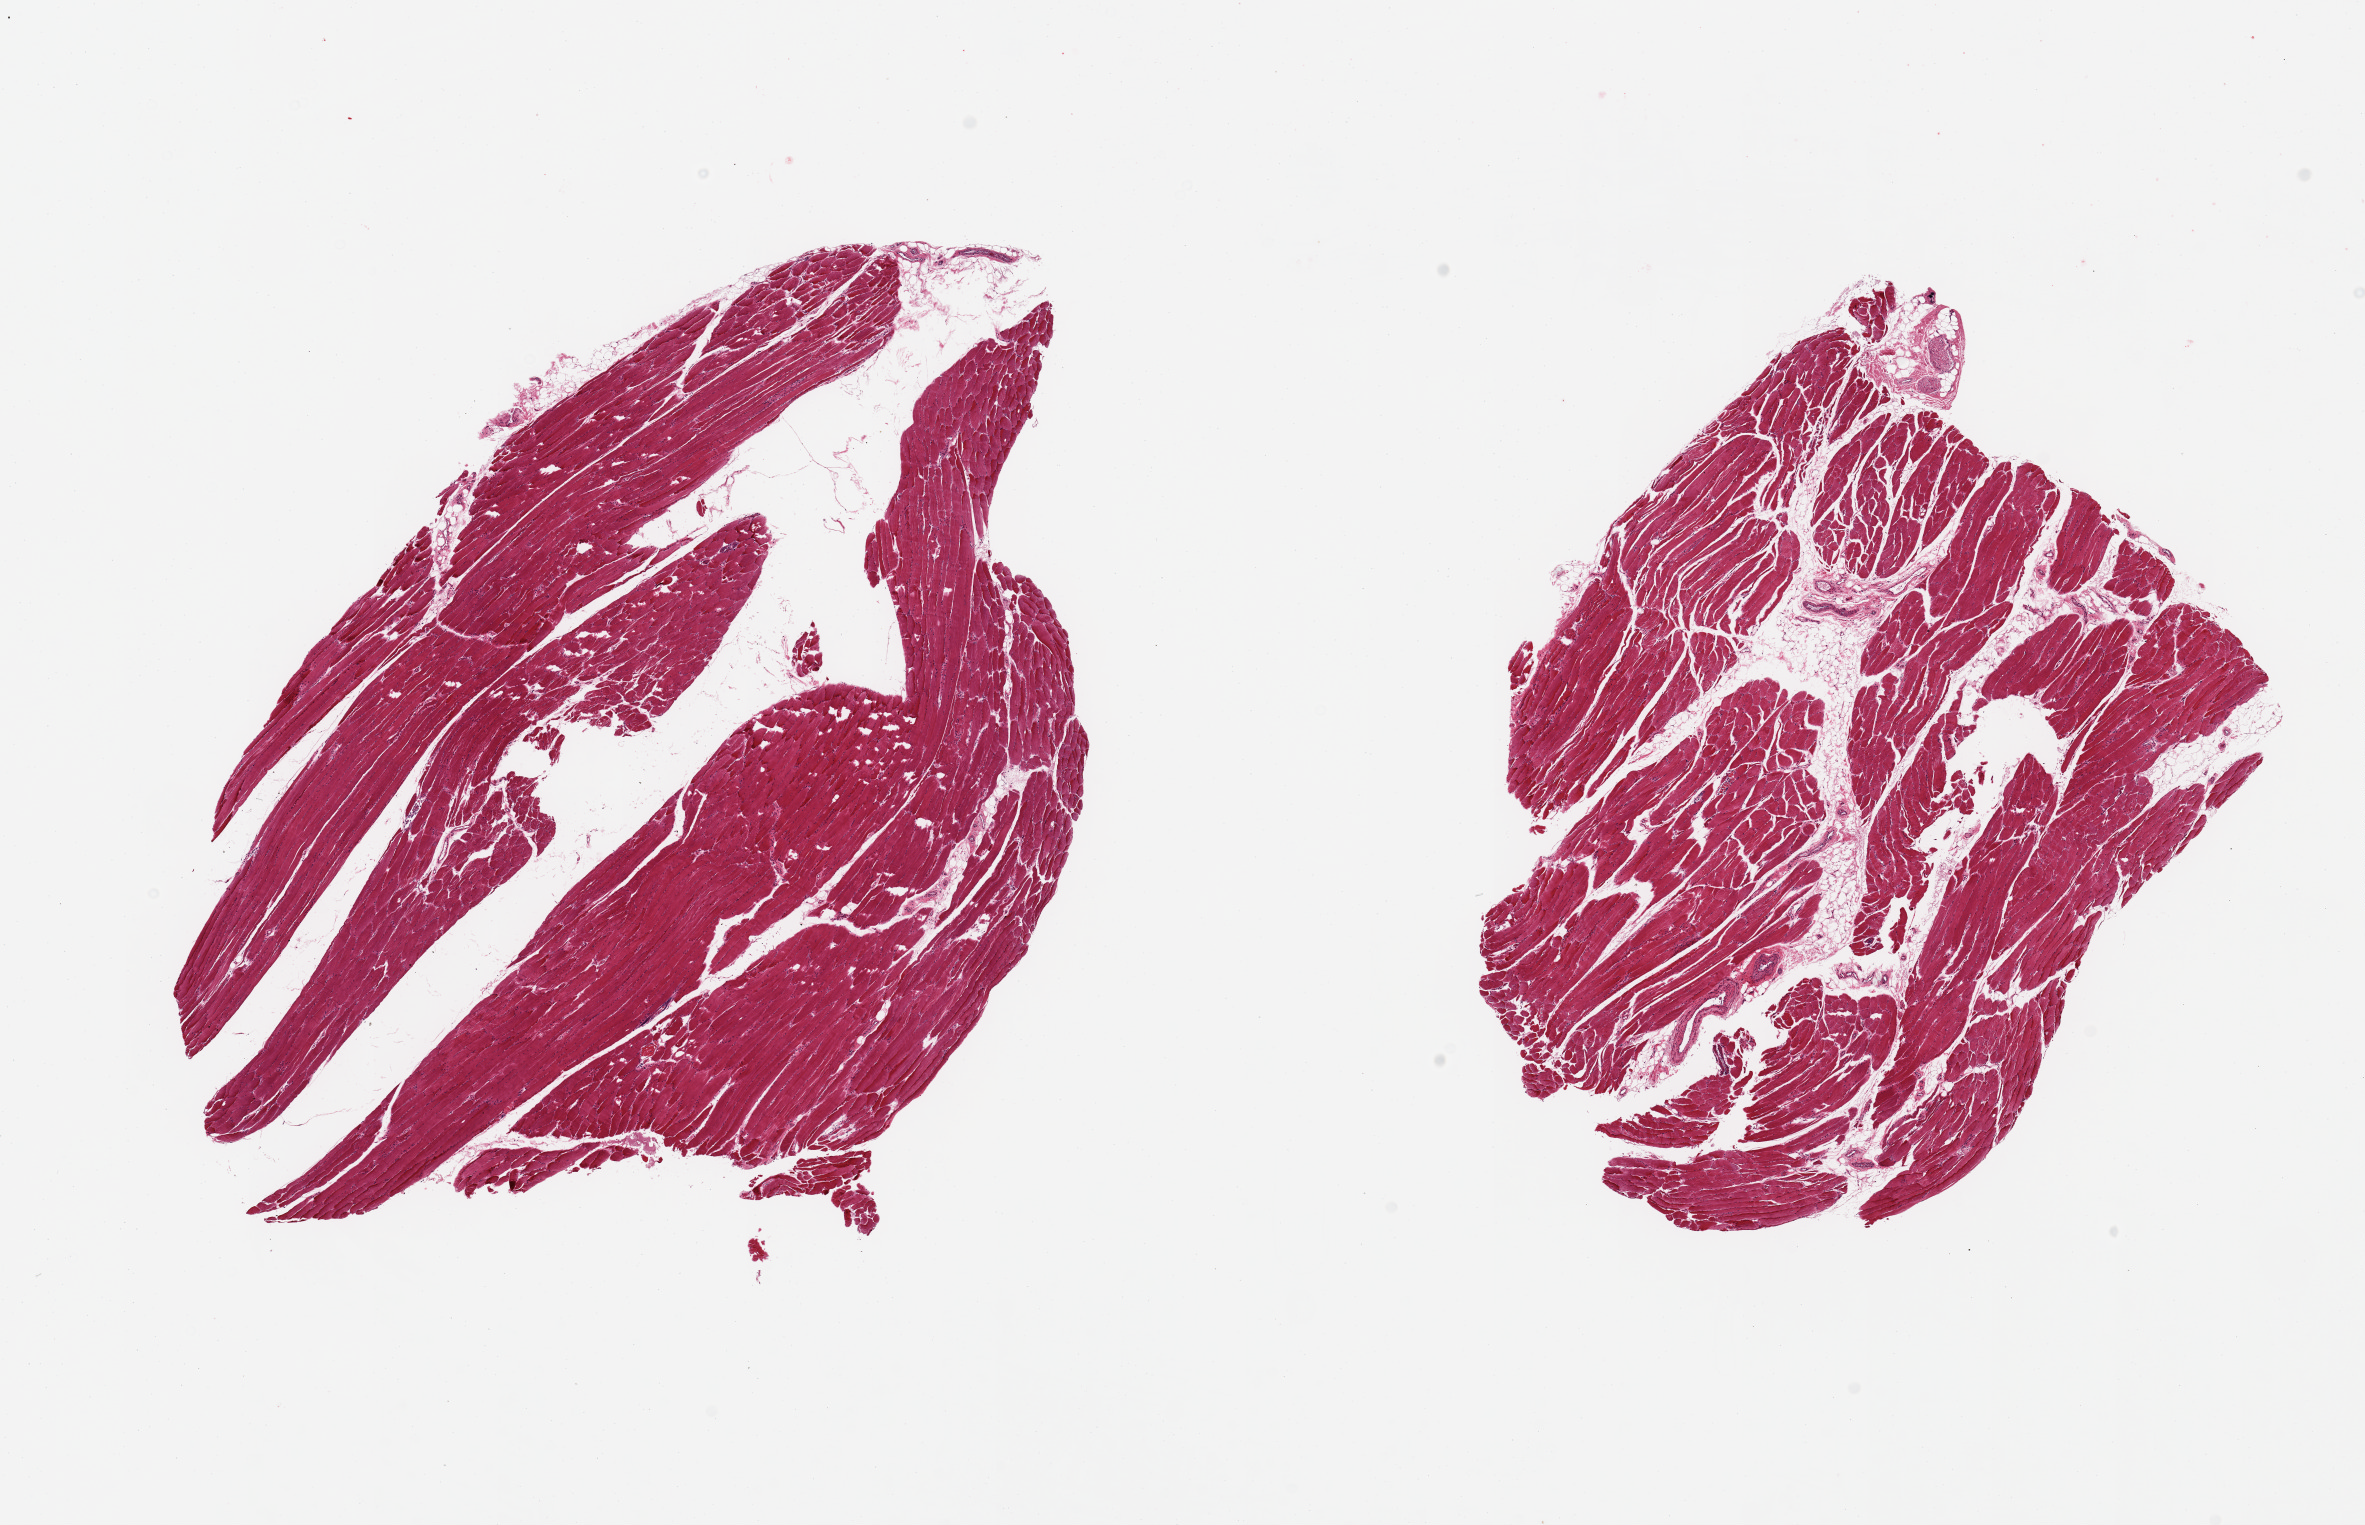
Digitized H&E-stained section, a low-resolution overview of the entire scanned area, about 18.7 x 12.1 mm (acquisition: 20x scan); PAXgene-fixed paraffin-embedded (PFPE) section; section of skeletal muscle (target tissue); tissue donor sample. Donor sex: male.
• pathologist's review note for this sample: 2 pieces, 20-25% interstitial fat